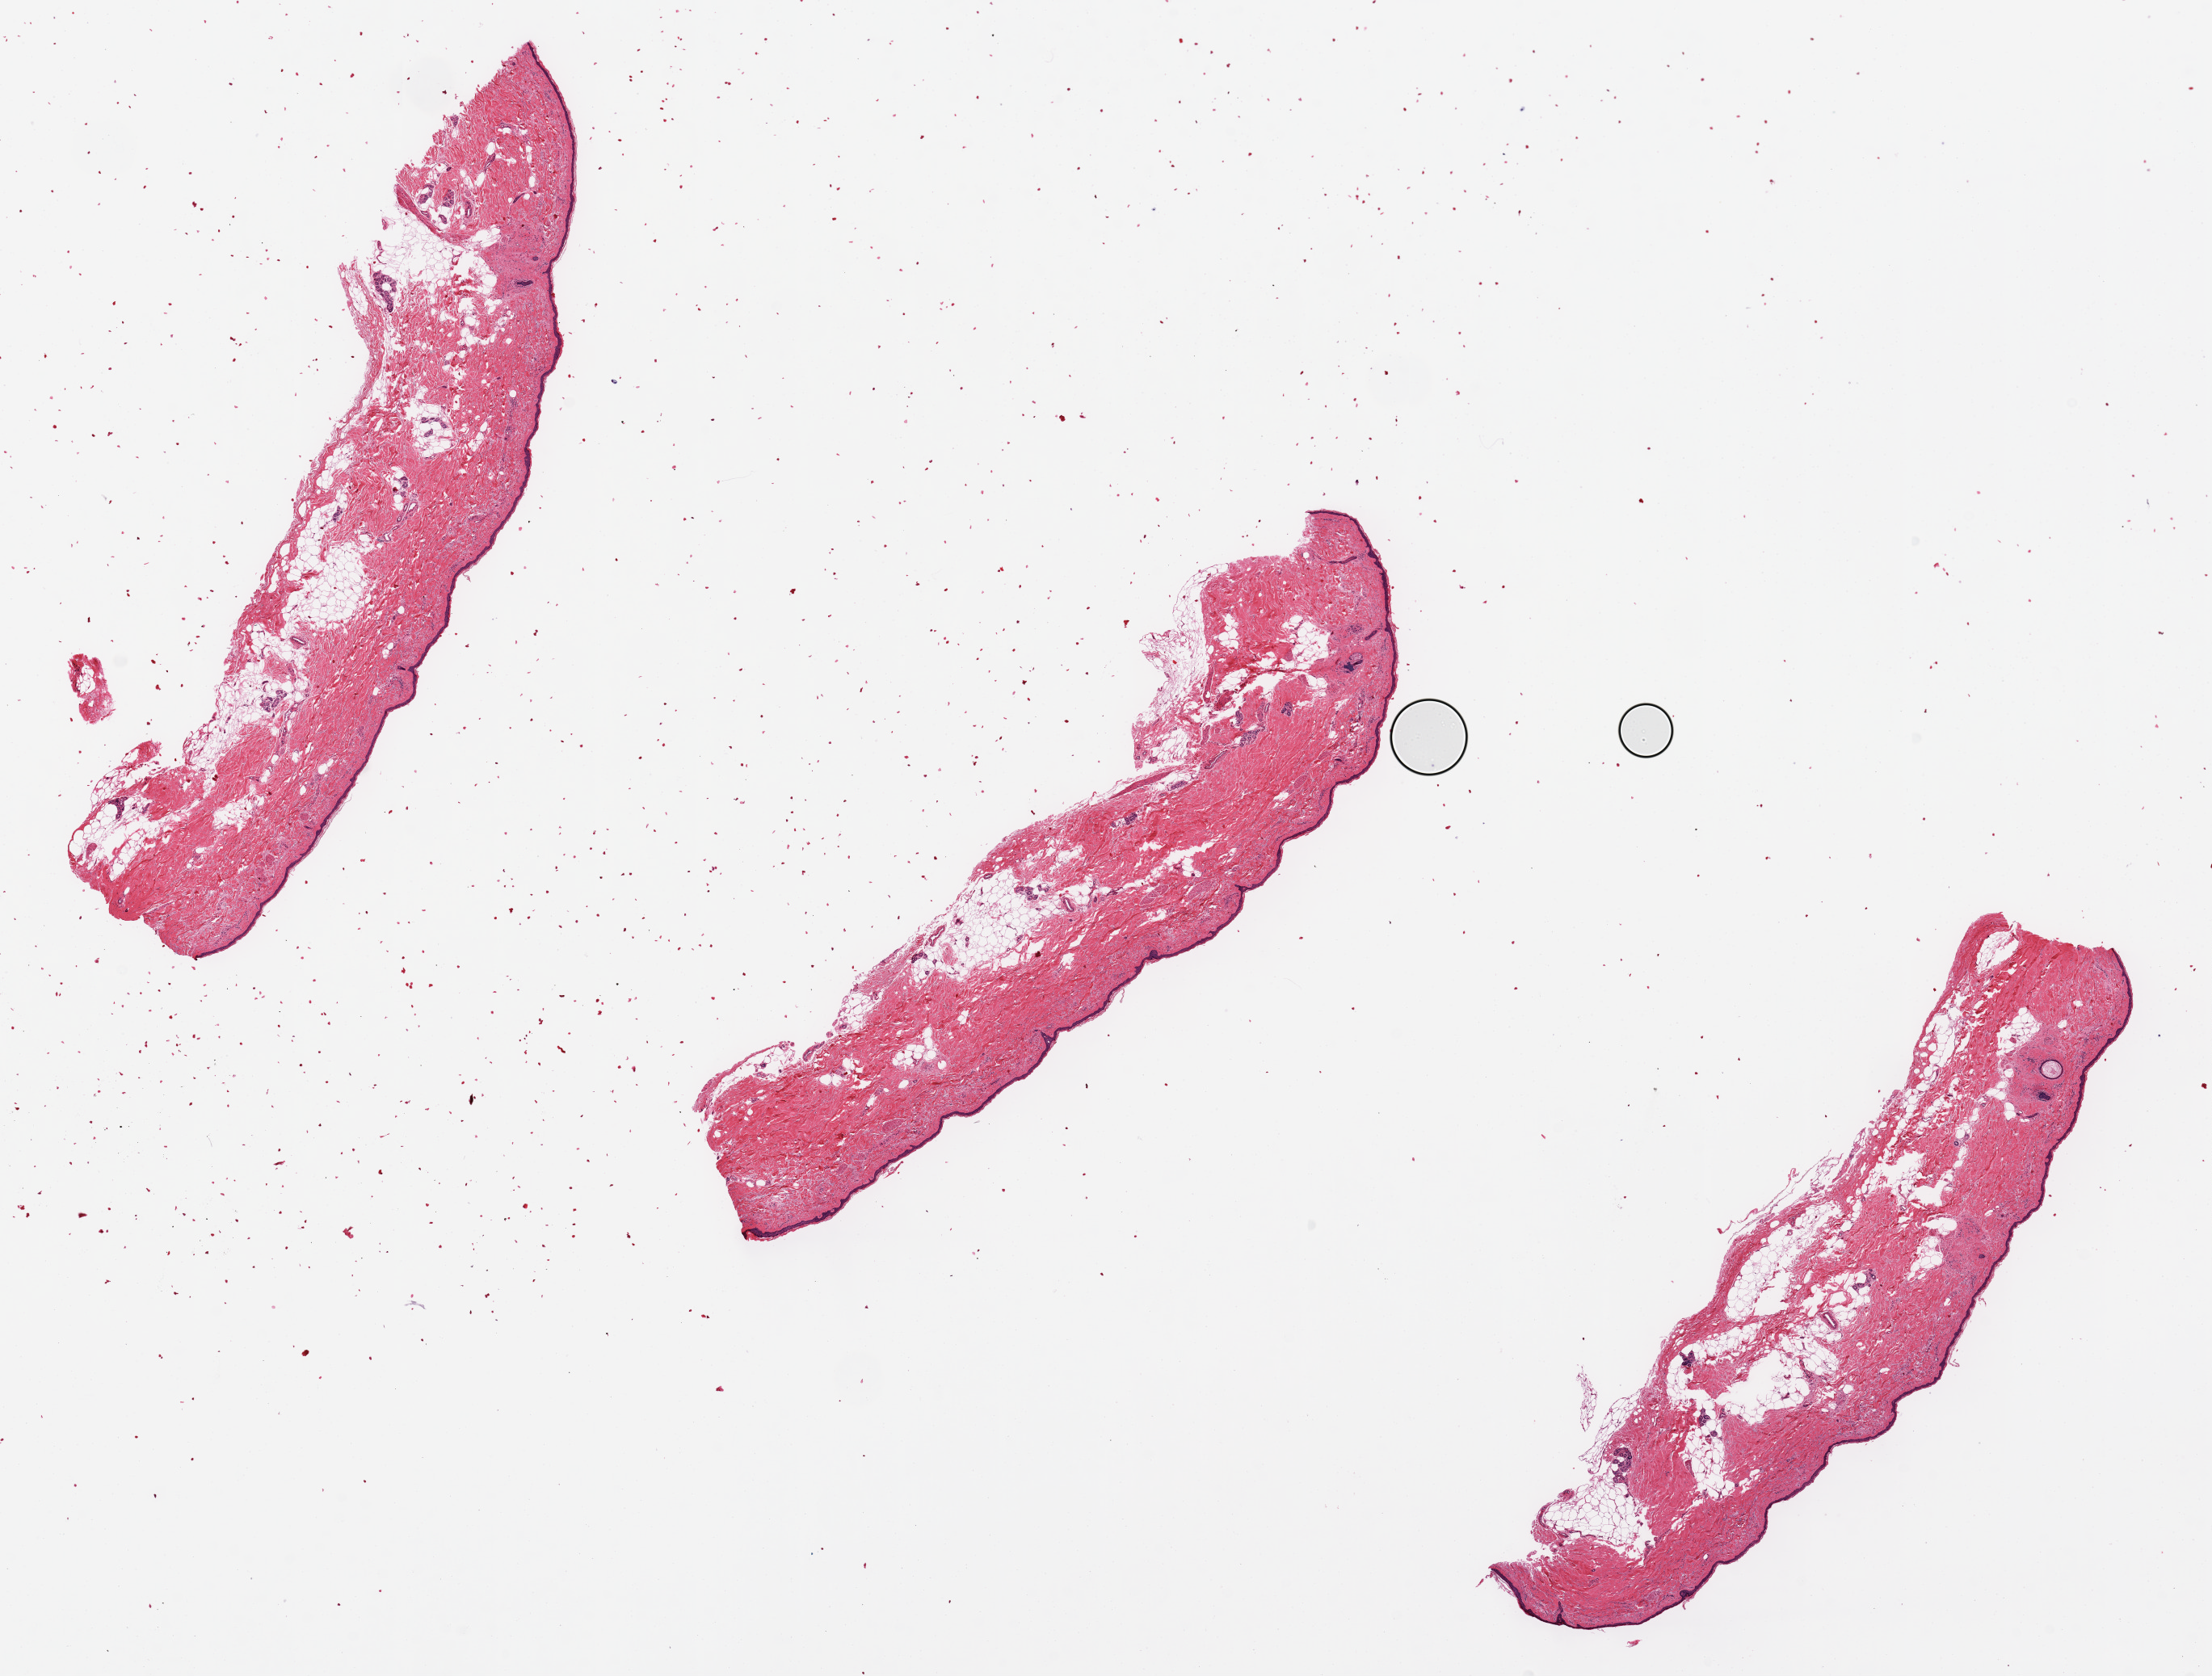
H&E whole-slide image — low-resolution overview of the scanned area, about 21.7 x 16.4 mm. PAXgene-fixed paraffin-embedded (PFPE) section. Target tissue: skin of lower leg. Tissue donor sample.
- reviewer comment on this tissue sample: 3 pieces 9.5x1.8mm. Epidermis 30um